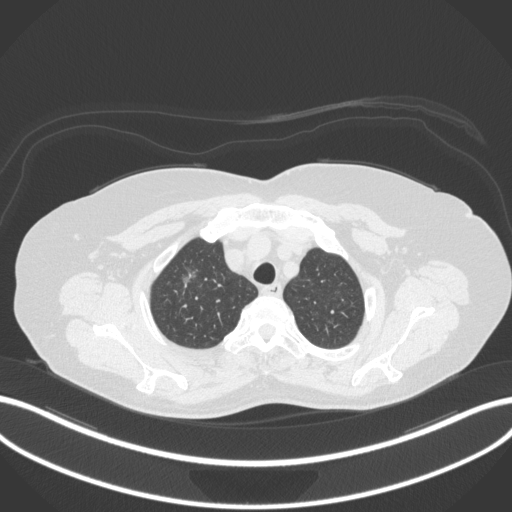
Chest CT, one axial slice; position 297 of 365 along the scan axis; reconstruction kernel B31f; 120 kVp; lung window (W 1500 / L -600 HU); 1 mm slice thickness; 512 × 512 image matrix. Patient: female, 62 years. From the clinical record (not read from this slice): clinical TNM (as recorded): T1c N0 M0.
Structures marked on this image (bounding box drawn by a radiologist):
- lung tumour (recorded histology: adenocarcinoma): bounding box [x1, y1, x2, y2] px = [176, 258, 207, 289]